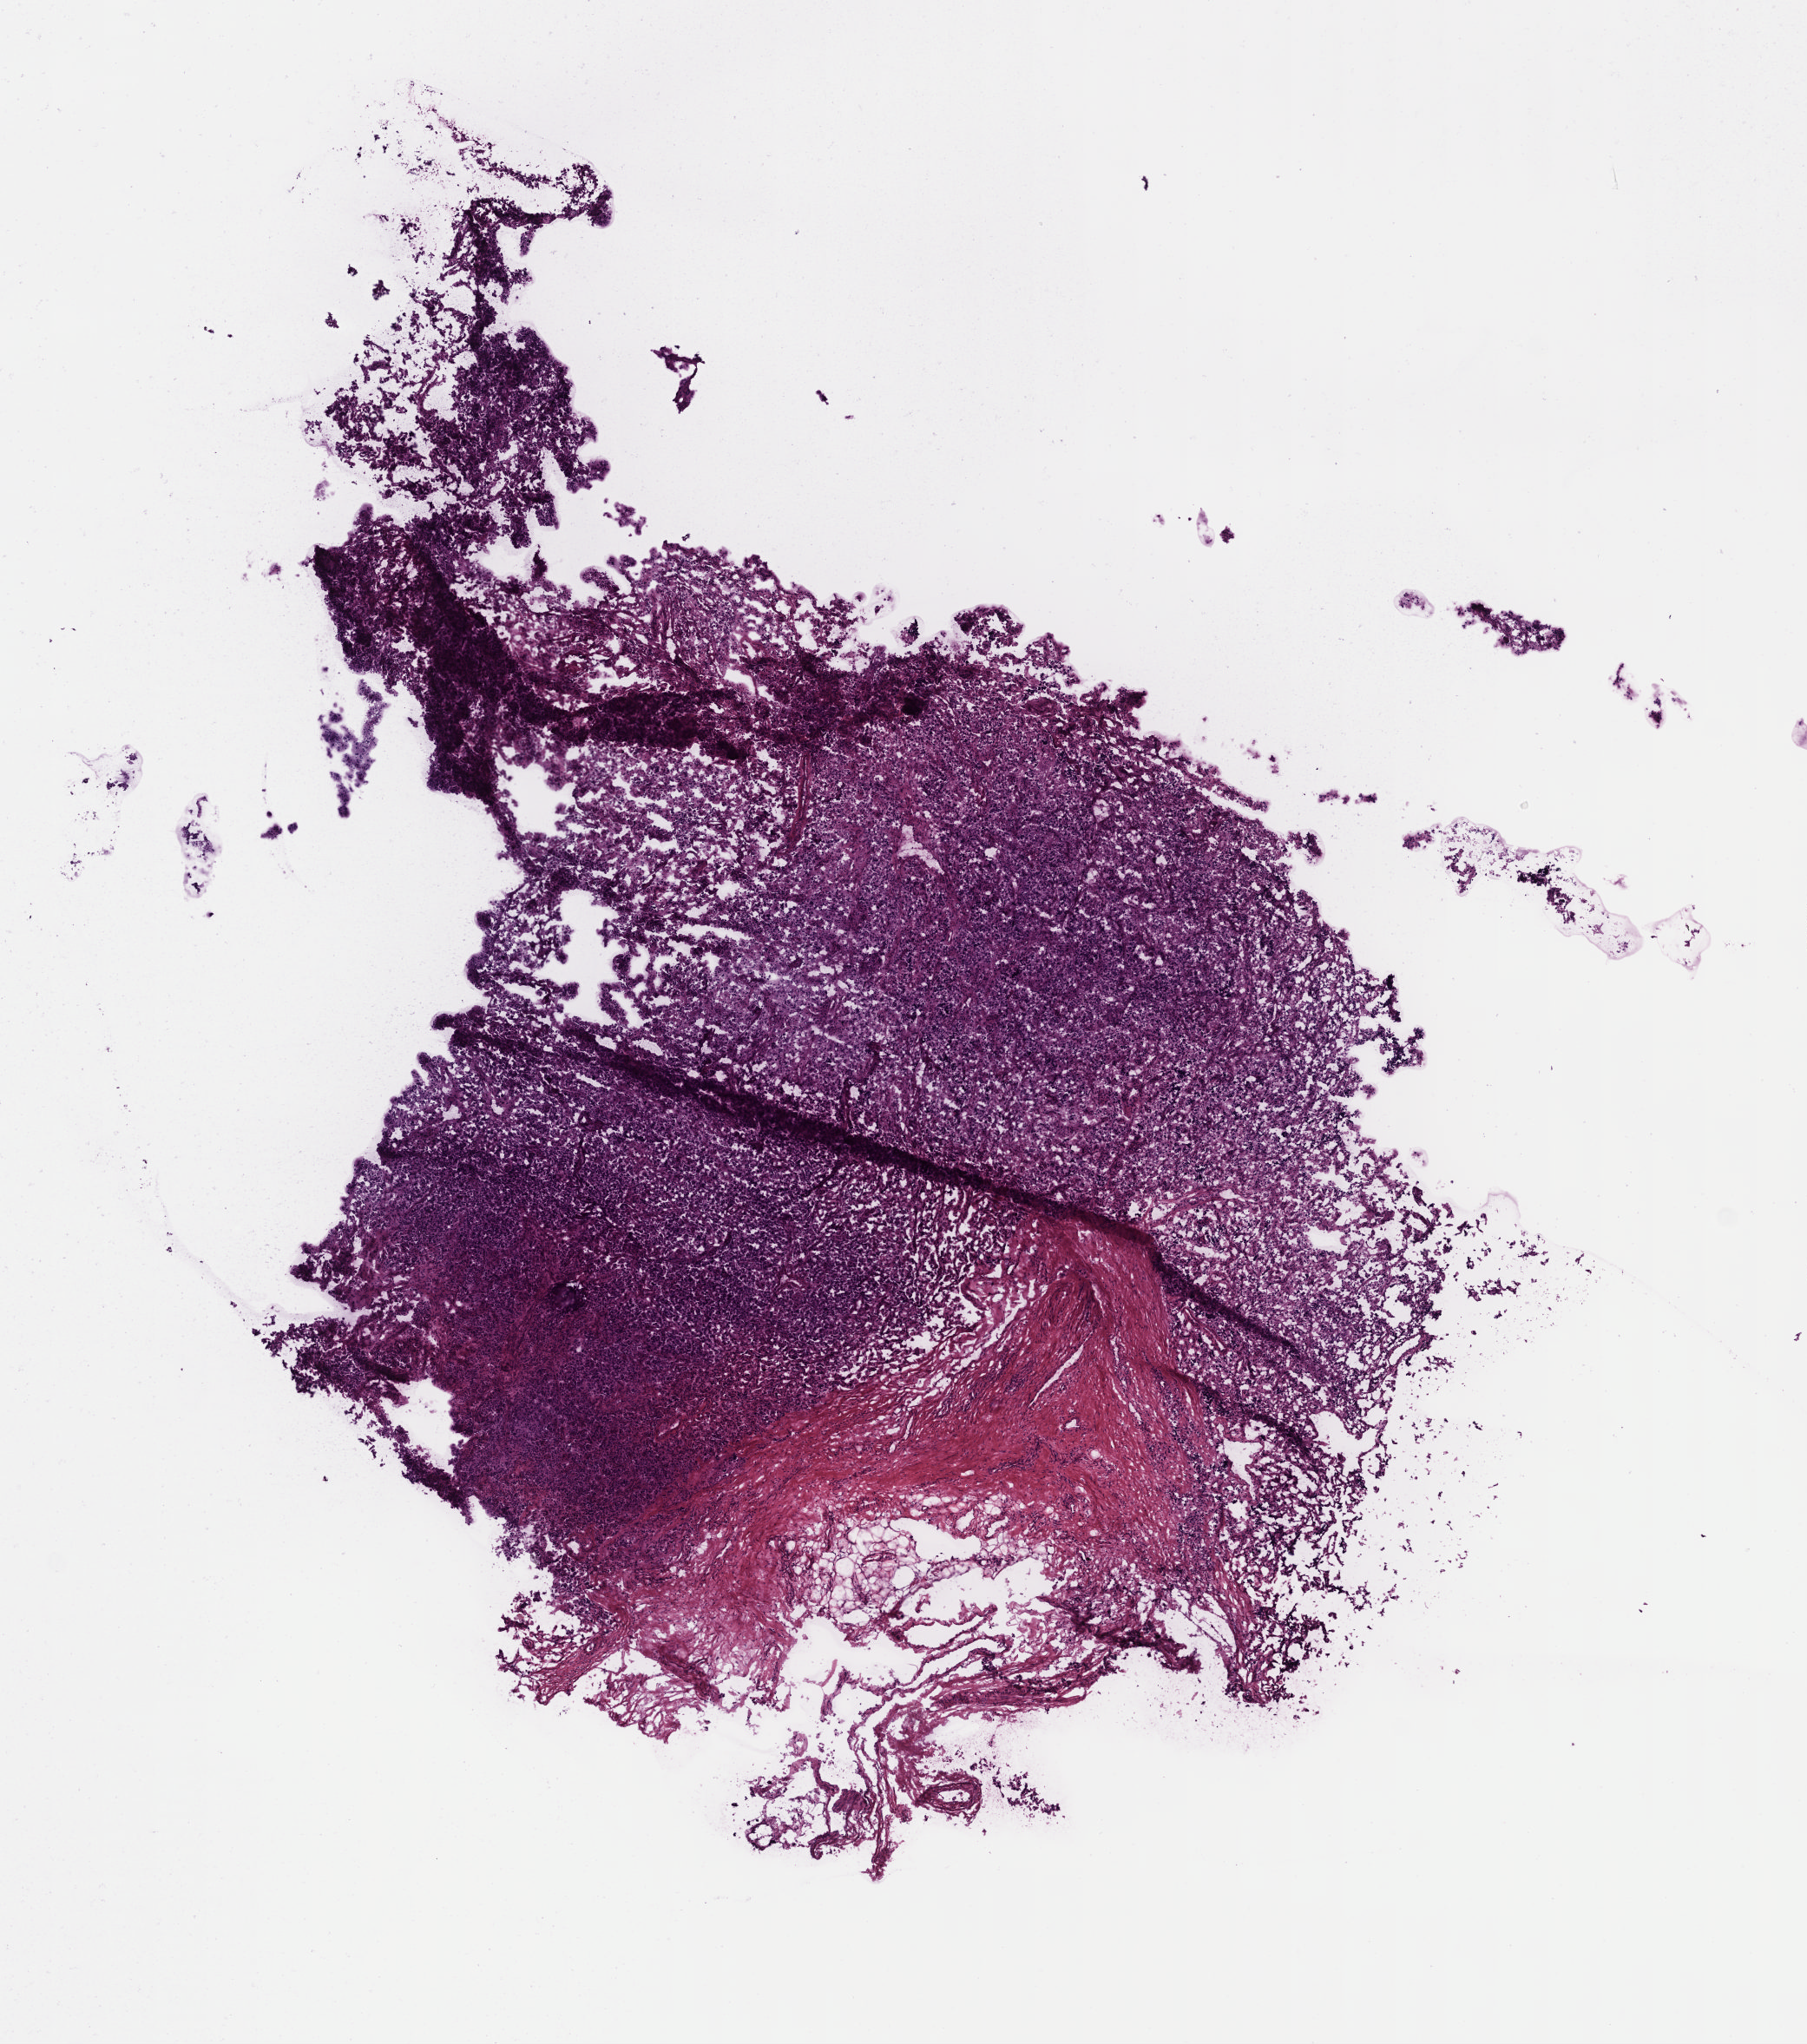
Whole-slide histology image, Hematoxylin and eosin (H&E) stained — whole scanned area (about 8.2 x 9.3 mm, slide scanned at 40x) shown as a low-resolution overview; frozen section from the top of the tissue portion; primary tumour sample from the retroperitoneum and peritoneum. Patient: male, age at initial diagnosis 41 years. Pathologist review of this section (percent, as recorded): tumour cells 80%, tumour nuclei 80%.
Pathologic diagnosis: Extra-adrenal paraganglioma, malignant (retroperitoneum).